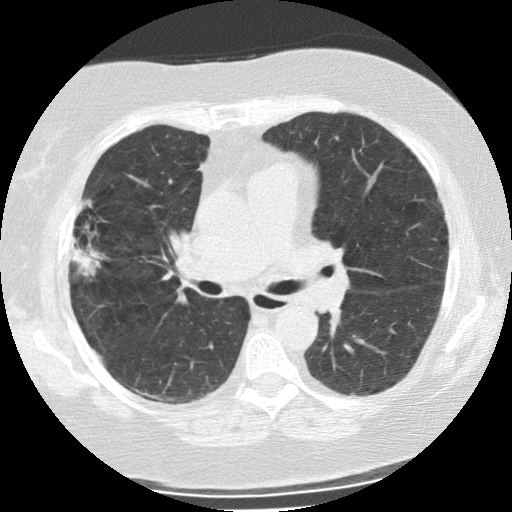
Chest CT (low-dose screening protocol), one axial image; second screening round (one year after baseline); lung window (W 1500 / L -600 HU); 120 kVp; slice 91 of 225 in the series; 512 × 512 image matrix, field of view 320 × 320 mm. Female participant, aged 73 years at enrolment.
- Lesion marked by an expert reader, bounding box [x1, y1, x2, y2] px = [56, 204, 107, 279].
- The screening reader recorded 2 non-calcified nodules or masses ≥4 mm on this exam (right upper lobe, left upper lobe); which of them this box marks is not recorded.
- Official screen result: positive, change unspecified: nodule(s) >= 4 mm or enlarging nodule(s), mass(es), or other non-specific abnormalities suspicious for lung cancer.
- Later outcome: lung cancer diagnosed 47 days after this screen — bronchiolo-alveolar adenocarcinoma, NOS, right upper lobe, moderately differentiated (G2), stage IIIB (AJCC 6th edition), 21 mm at pathology.